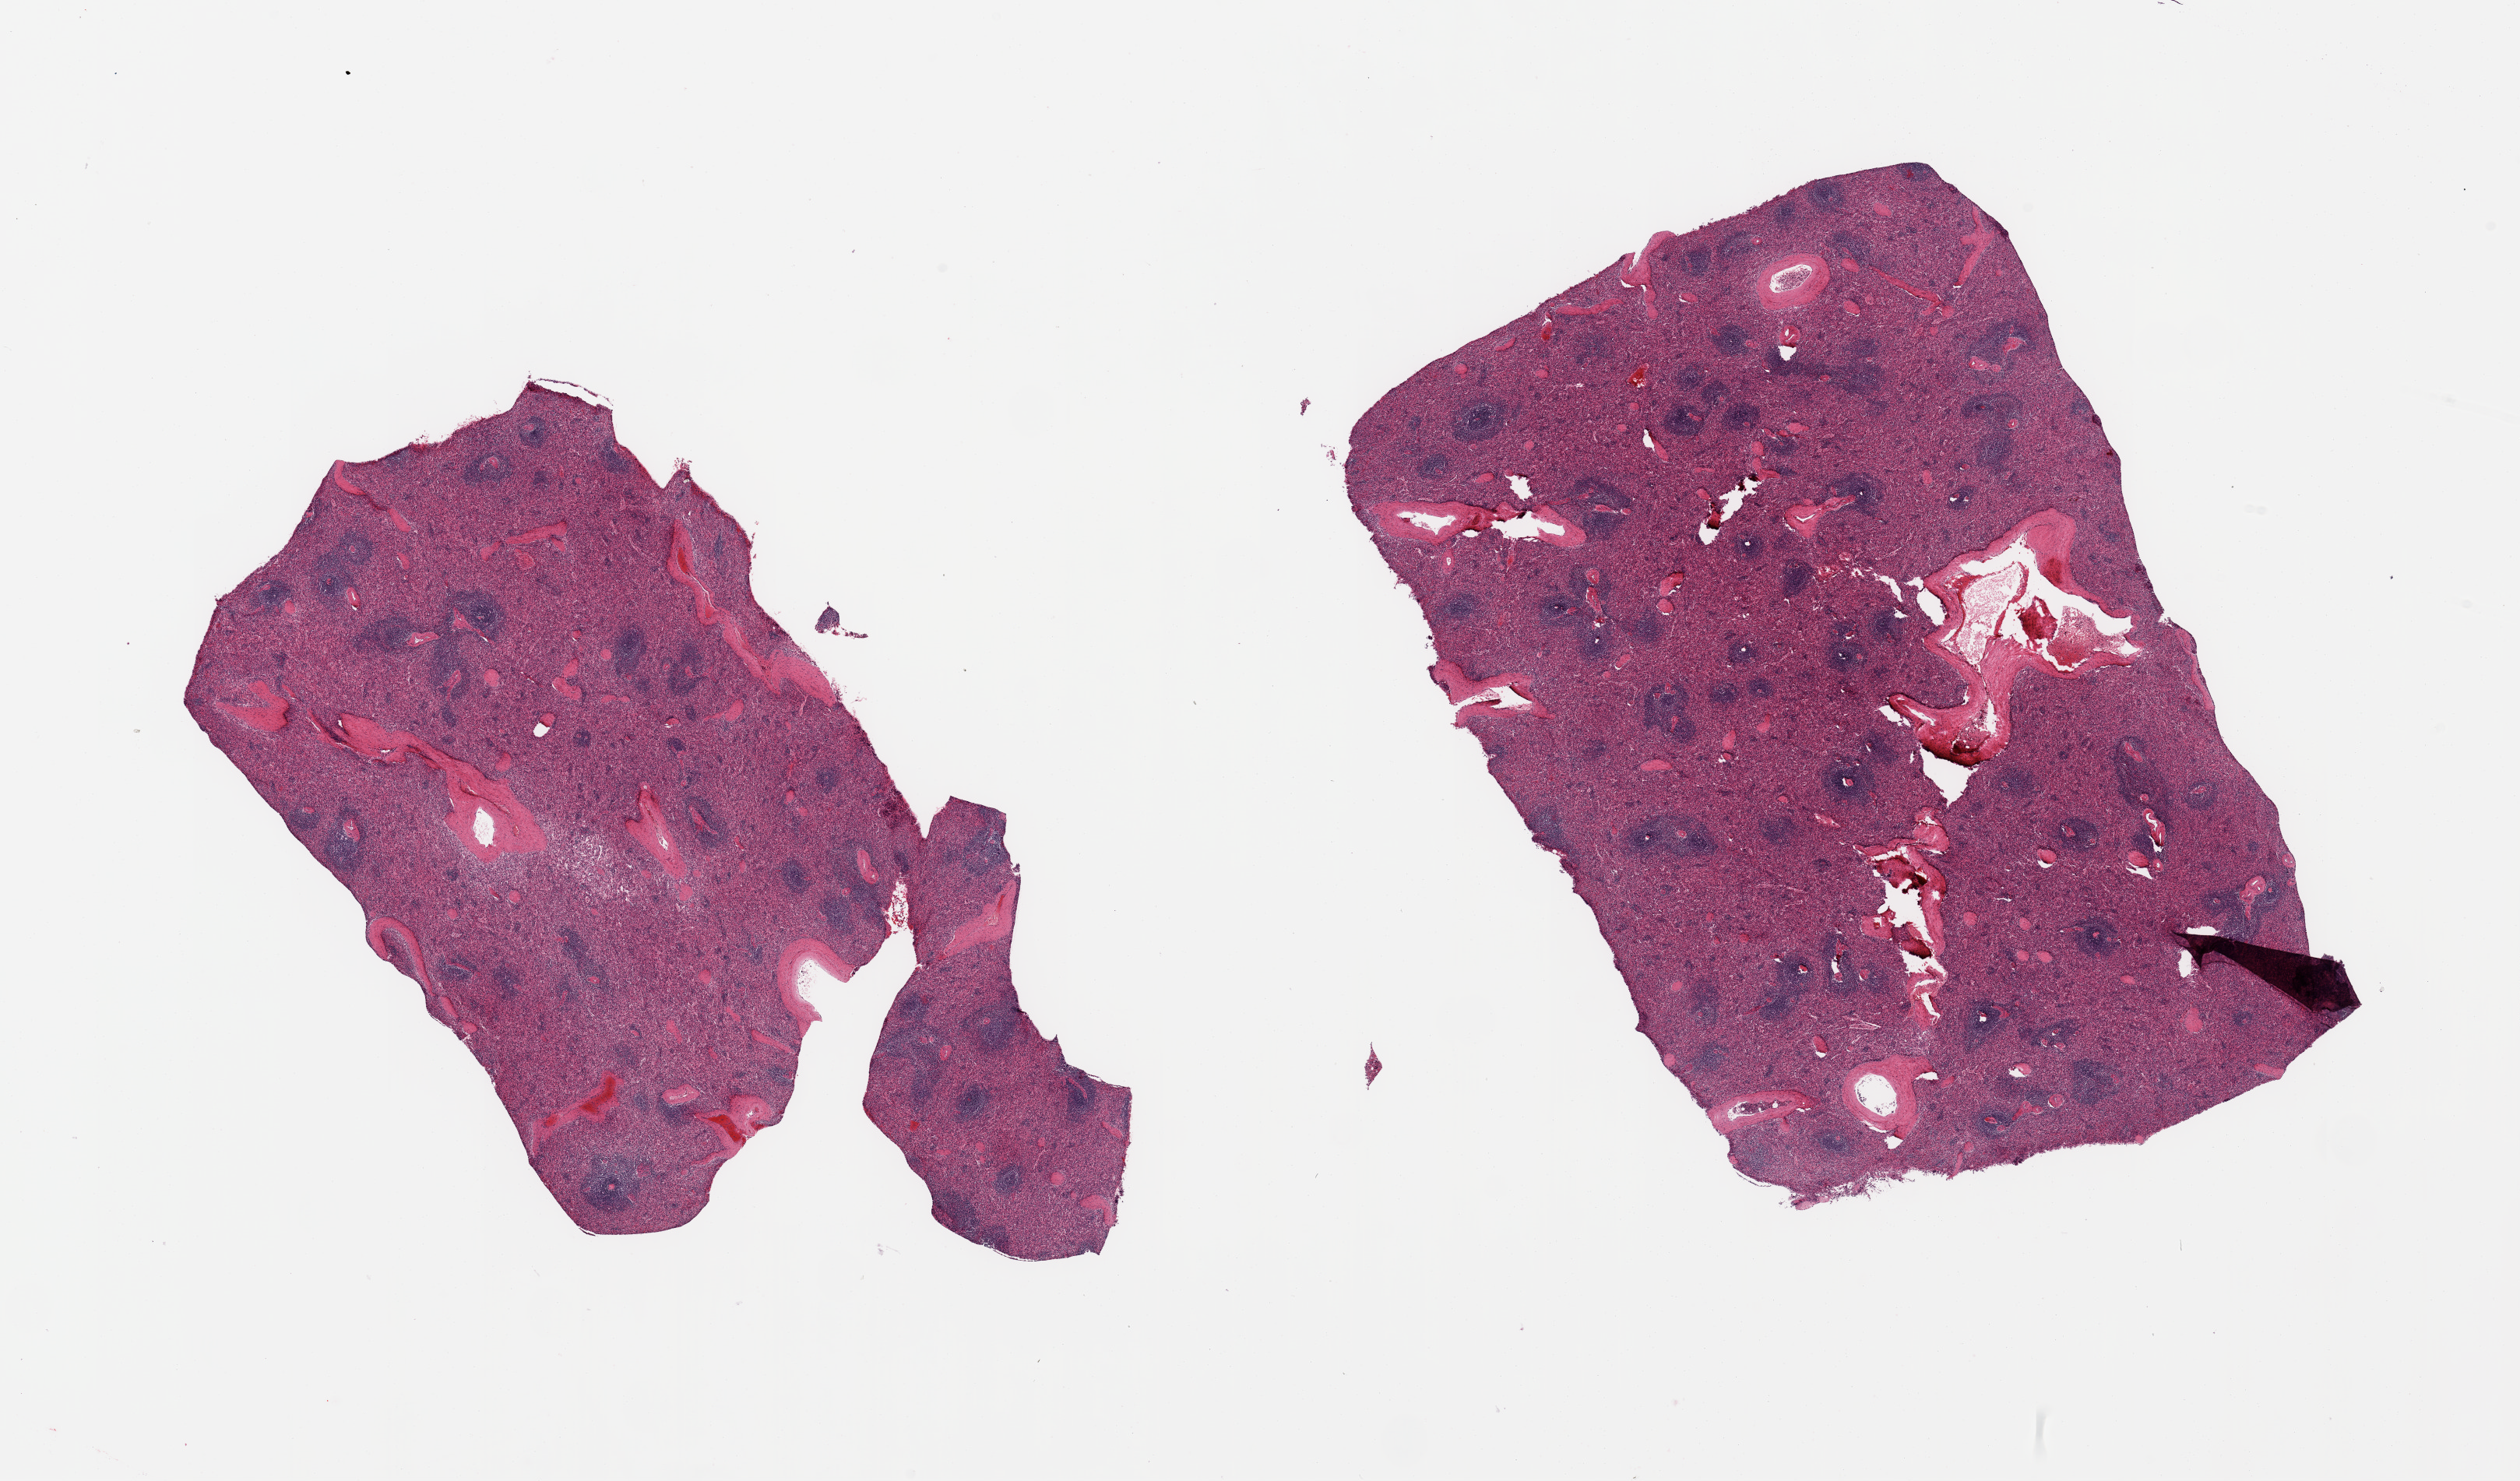
Haematoxylin and eosin whole-slide image — a low-resolution overview of the entire scanned area, about 25.6 x 15.0 mm (slide scanned at 20x), PAXgene-fixed, paraffin-embedded tissue, target tissue: spleen, donor tissue sample. Donor: male.
Review note (as recorded): 2 pieces, no abnormalities.